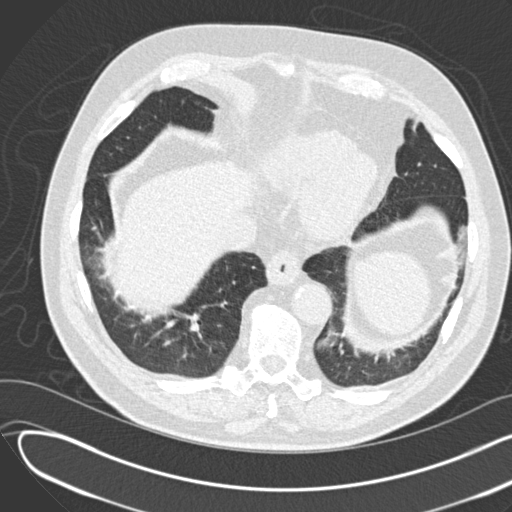
Low-dose screening chest CT, one axial slice; position 31 of 155 along the scan axis; lung window (W 1500 / L -600 HU); 512 × 512 image matrix, field of view 380 × 380 mm.
Structures marked on this image (outlined manually by an expert reader):
- lesion 1 (tumor, lower lobe of right lung): box from (x=198, y=332) to (x=202, y=338) px